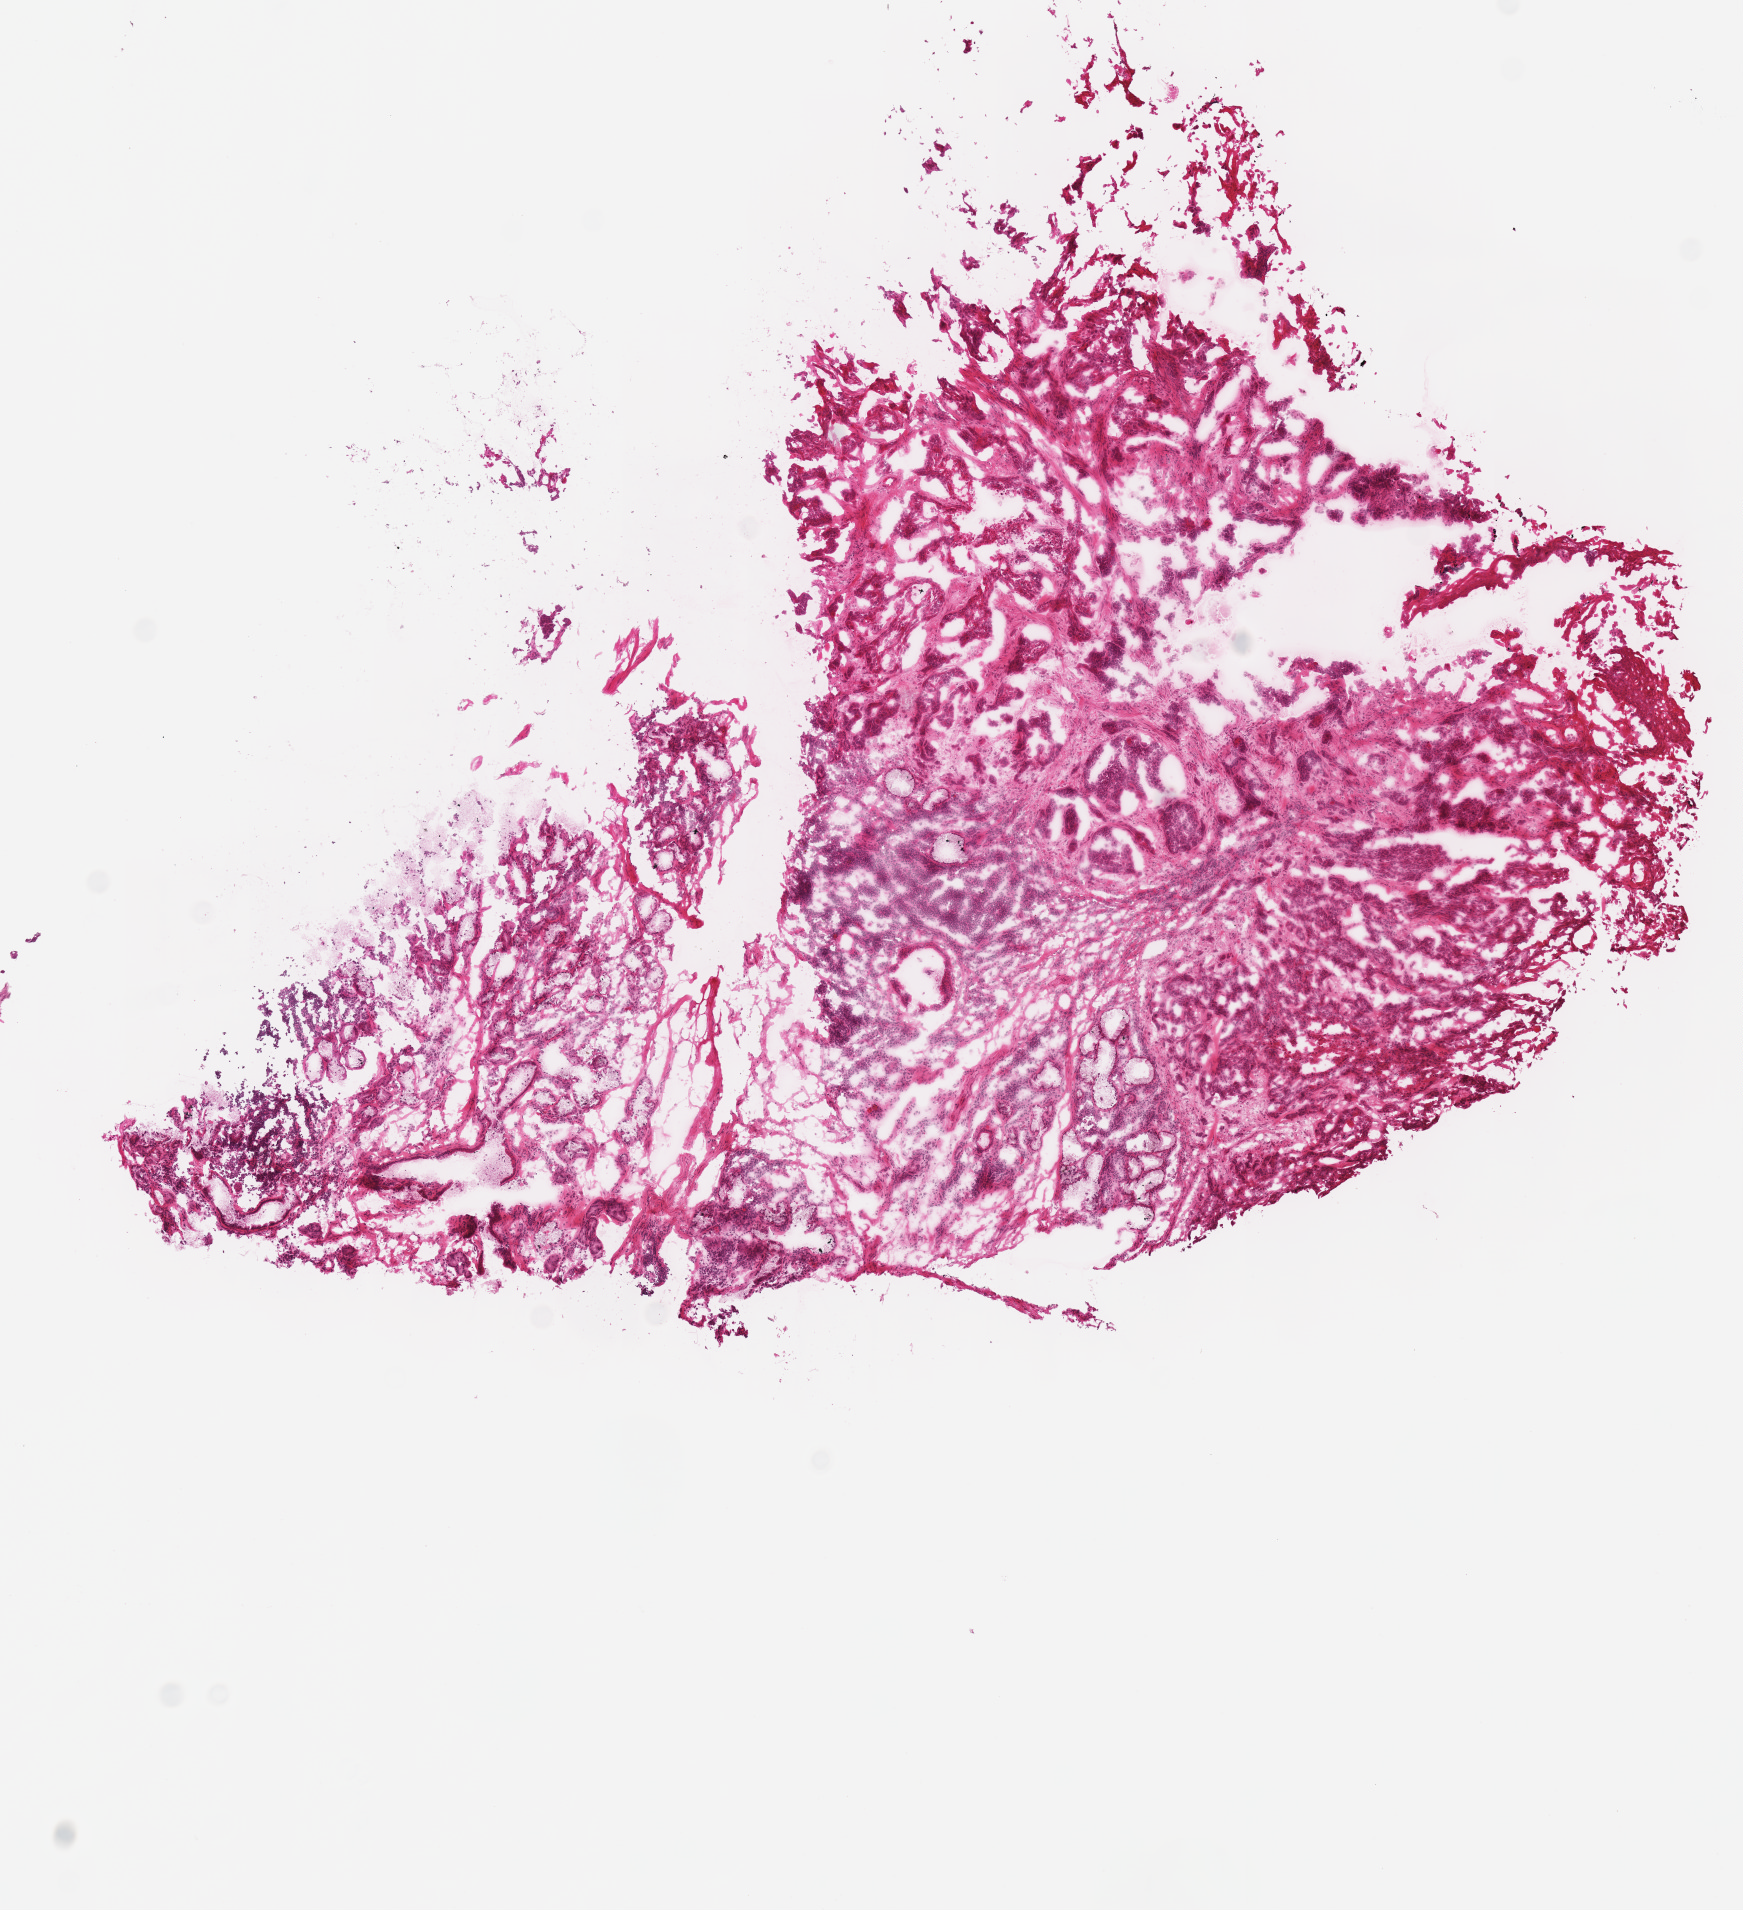
Whole-slide histology image, Hematoxylin and eosin (H&E) stained, whole scanned area (about 6.9 x 7.5 mm, acquisition: 40x scan) shown as a low-resolution overview, frozen section from the top of the tissue portion, sample: primary tumour, head and neck. Female, age 64 years at initial diagnosis. Histologic grade: G2 (moderately differentiated). Composition of this section per pathologist review: tumour cells 70%, tumour nuclei 75%, normal cells 0%, stromal cells 25%, necrosis 5%.
• AJCC pathologic stage: IVA (7th edition)
• histologic diagnosis: Squamous cell carcinoma, NOS